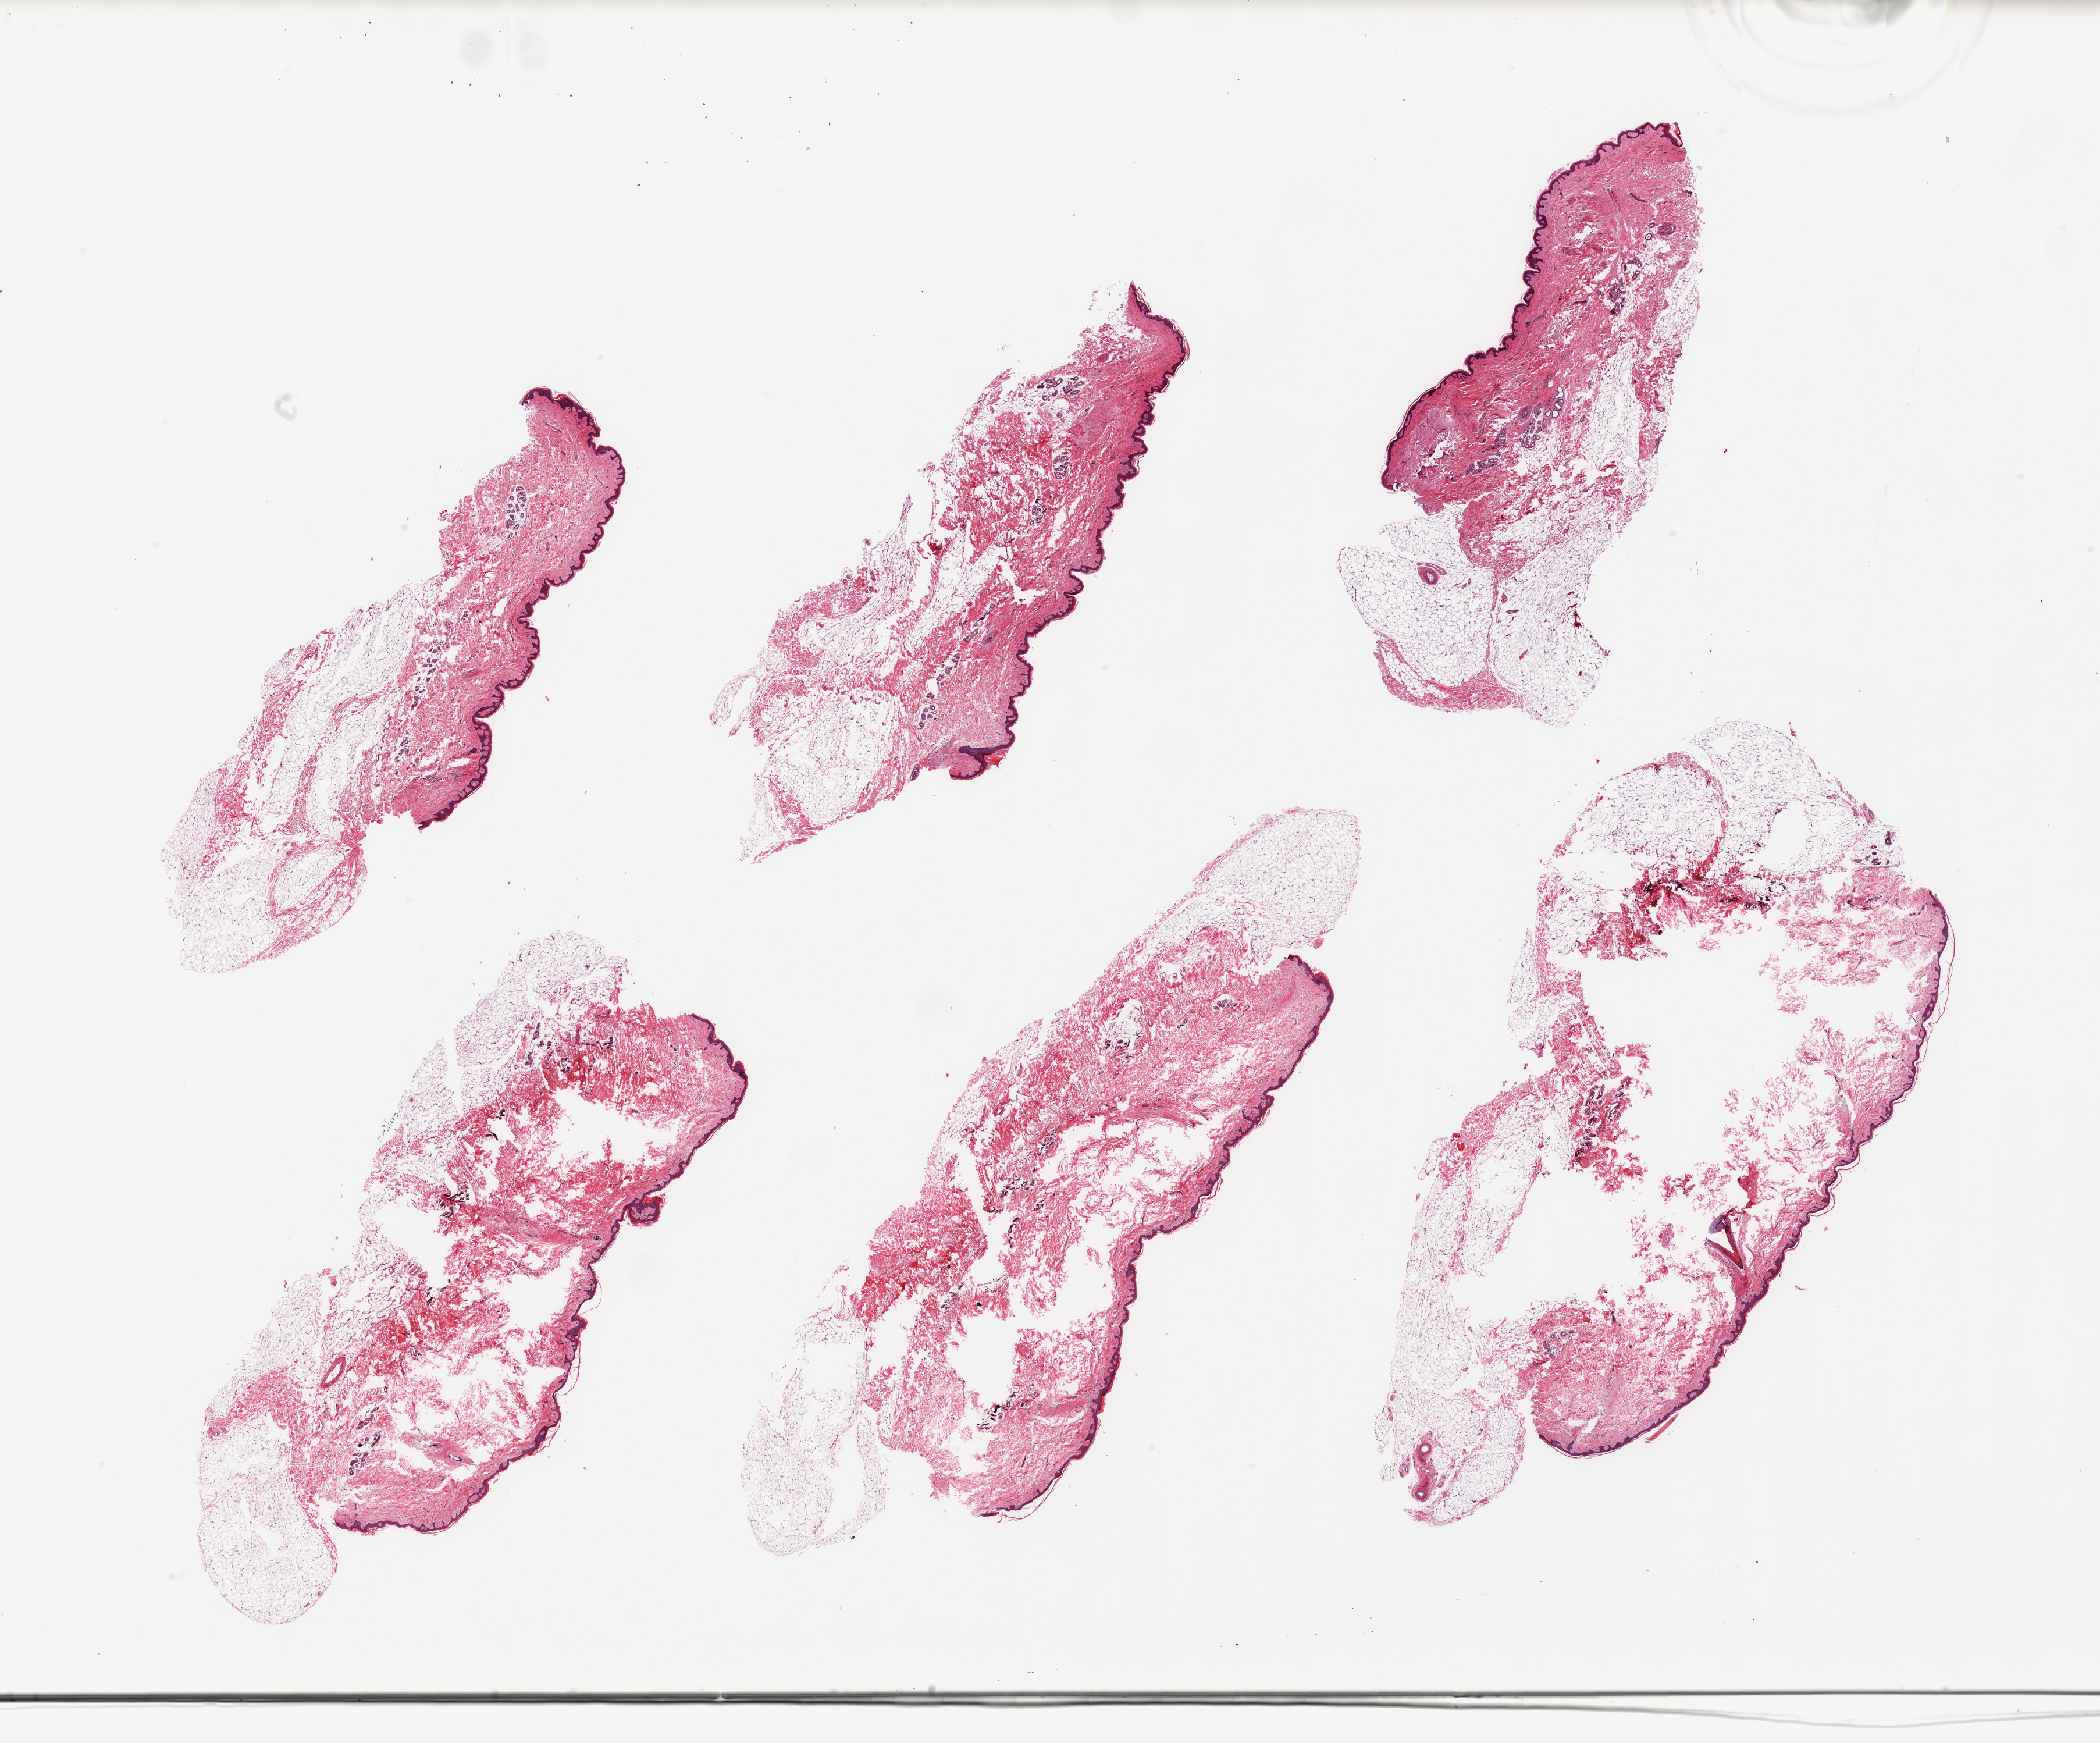
Digitized H&E-stained section, brightfield — shown as a low-resolution overview of the whole scanned area (about 28.5 x 23.7 mm, slide scanned at 20x). PAXgene-fixed paraffin-embedded (PFPE) section. Sampled site (target tissue): skin of suprapubic region. Donor tissue sample.
Review note (as recorded): 6 pieces; poorly trimmed with high fat content.